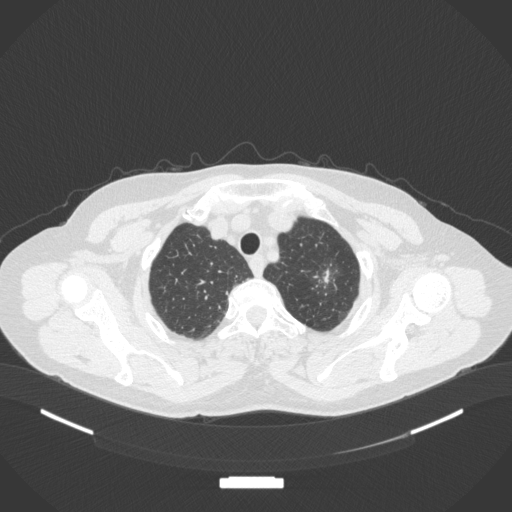
Chest CT, one axial slice; position 314 of 369 along the scan axis; reconstruction kernel B31f; 120 kVp; lung window (W 1500 / L -600 HU); 1 mm slice thickness; 512 × 512 image matrix, field of view 400 × 400 mm. Patient: female, 64 years. Case-level facts recorded for this patient, not image findings: clinical TNM (as recorded): T1c N0 M0; histopathological grade: G1.
Outlined on this slice (bounding box drawn by a radiologist):
- lung tumour (recorded histology: adenocarcinoma): bounding box [x1, y1, x2, y2] px = [304, 255, 346, 301]